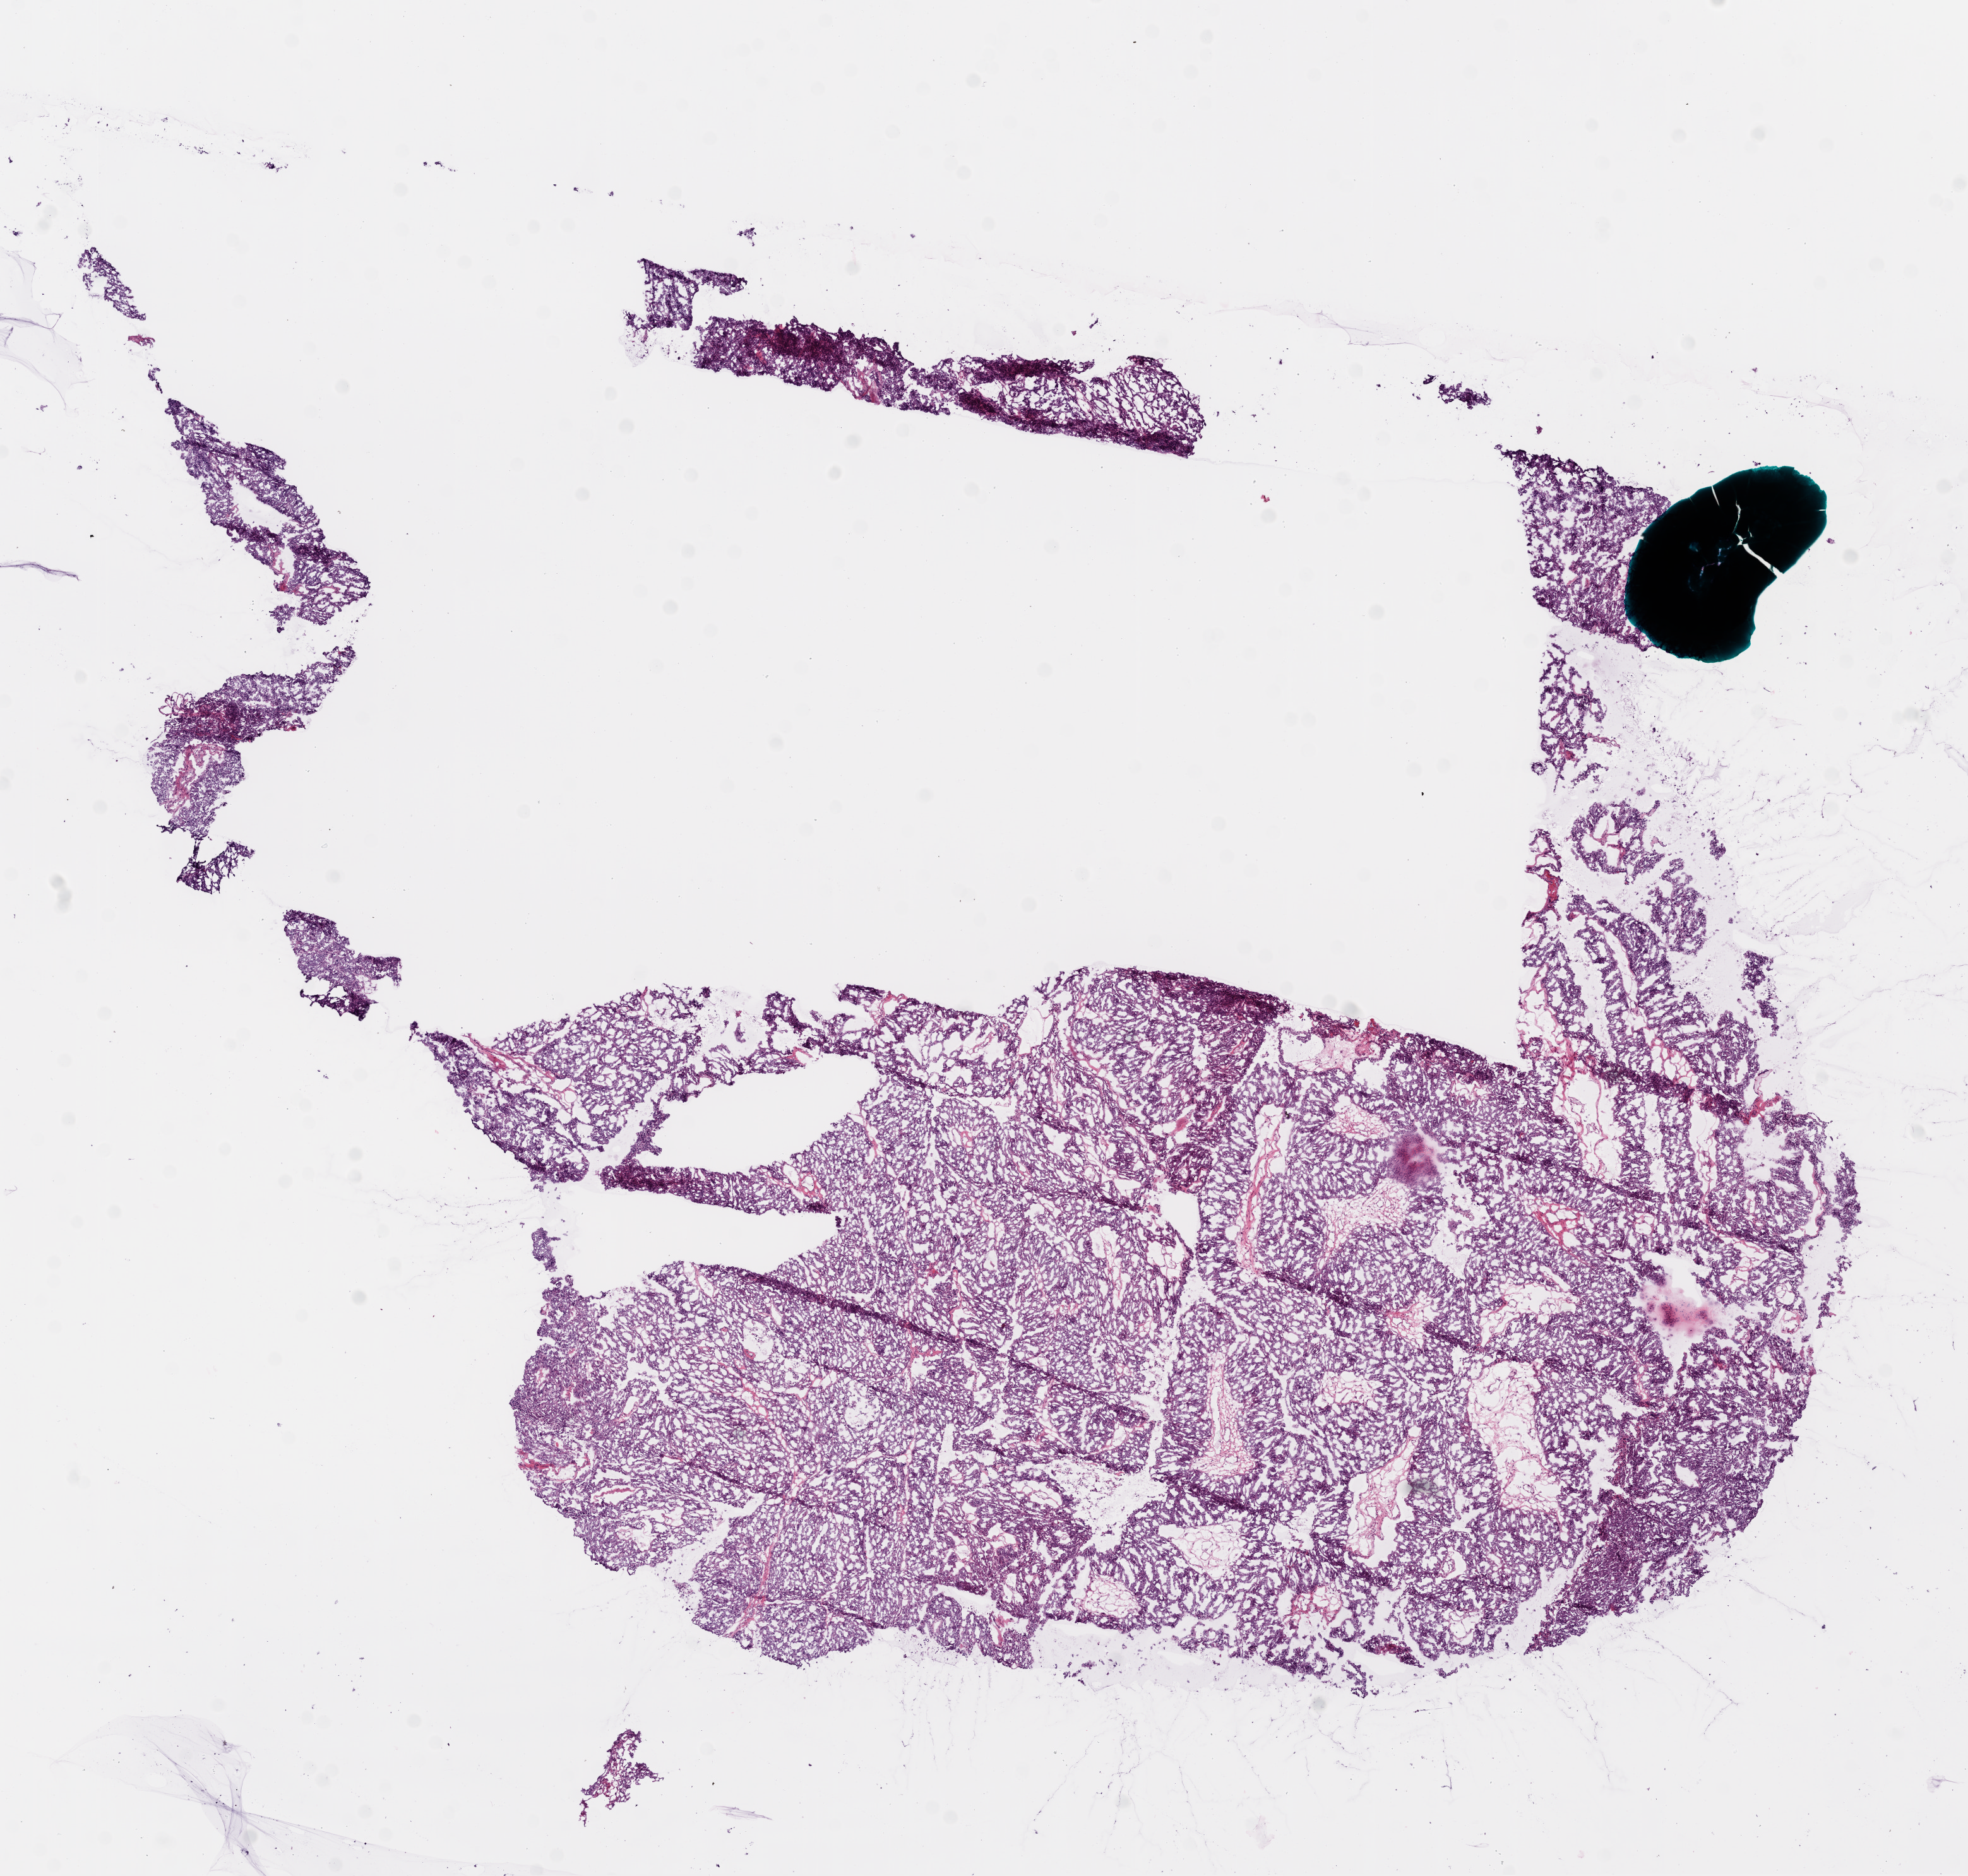
H&E whole-slide image, low-resolution overview of the scanned area, about 12.6 x 12.0 mm, frozen section, primary tumour sample from the ovary. Patient: female, age at initial diagnosis 46 years. Histologic grade: G3 (poorly differentiated). Slide review estimates, as recorded: tumour cells 94%, tumour nuclei 99%, normal cells 0%, stromal cells 5%, necrosis 1%.
• histologic diagnosis: Serous cystadenocarcinoma, NOS
• FIGO stage: IIIC
• laterality: bilateral